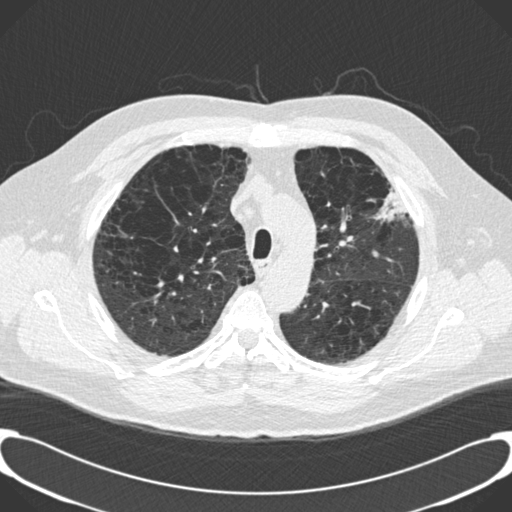
Axial slice from a low-dose chest CT screening exam. Third screening round (two years after baseline). Lung window (W 1500 / L -600 HU). 2 mm slice thickness. 120 kVp. 512 × 512 image matrix, field of view 380 × 380 mm. Male participant, aged 59 years at enrolment. Current smoker at enrolment.
Lesion marked by an expert reader, bounding box <361,164,414,226> (left, top, right, bottom; pixels). Screening reader's record for this exam: no non-calcified nodule ≥4 mm recorded. Official screen result: positive, other. Participant outcome: lung cancer diagnosed 134 days after this screen — bronchiolo-alveolar carcinoma, mixed mucinous and non-mucinous, left upper lobe, stage IA (AJCC 6th edition), 20 mm at pathology.